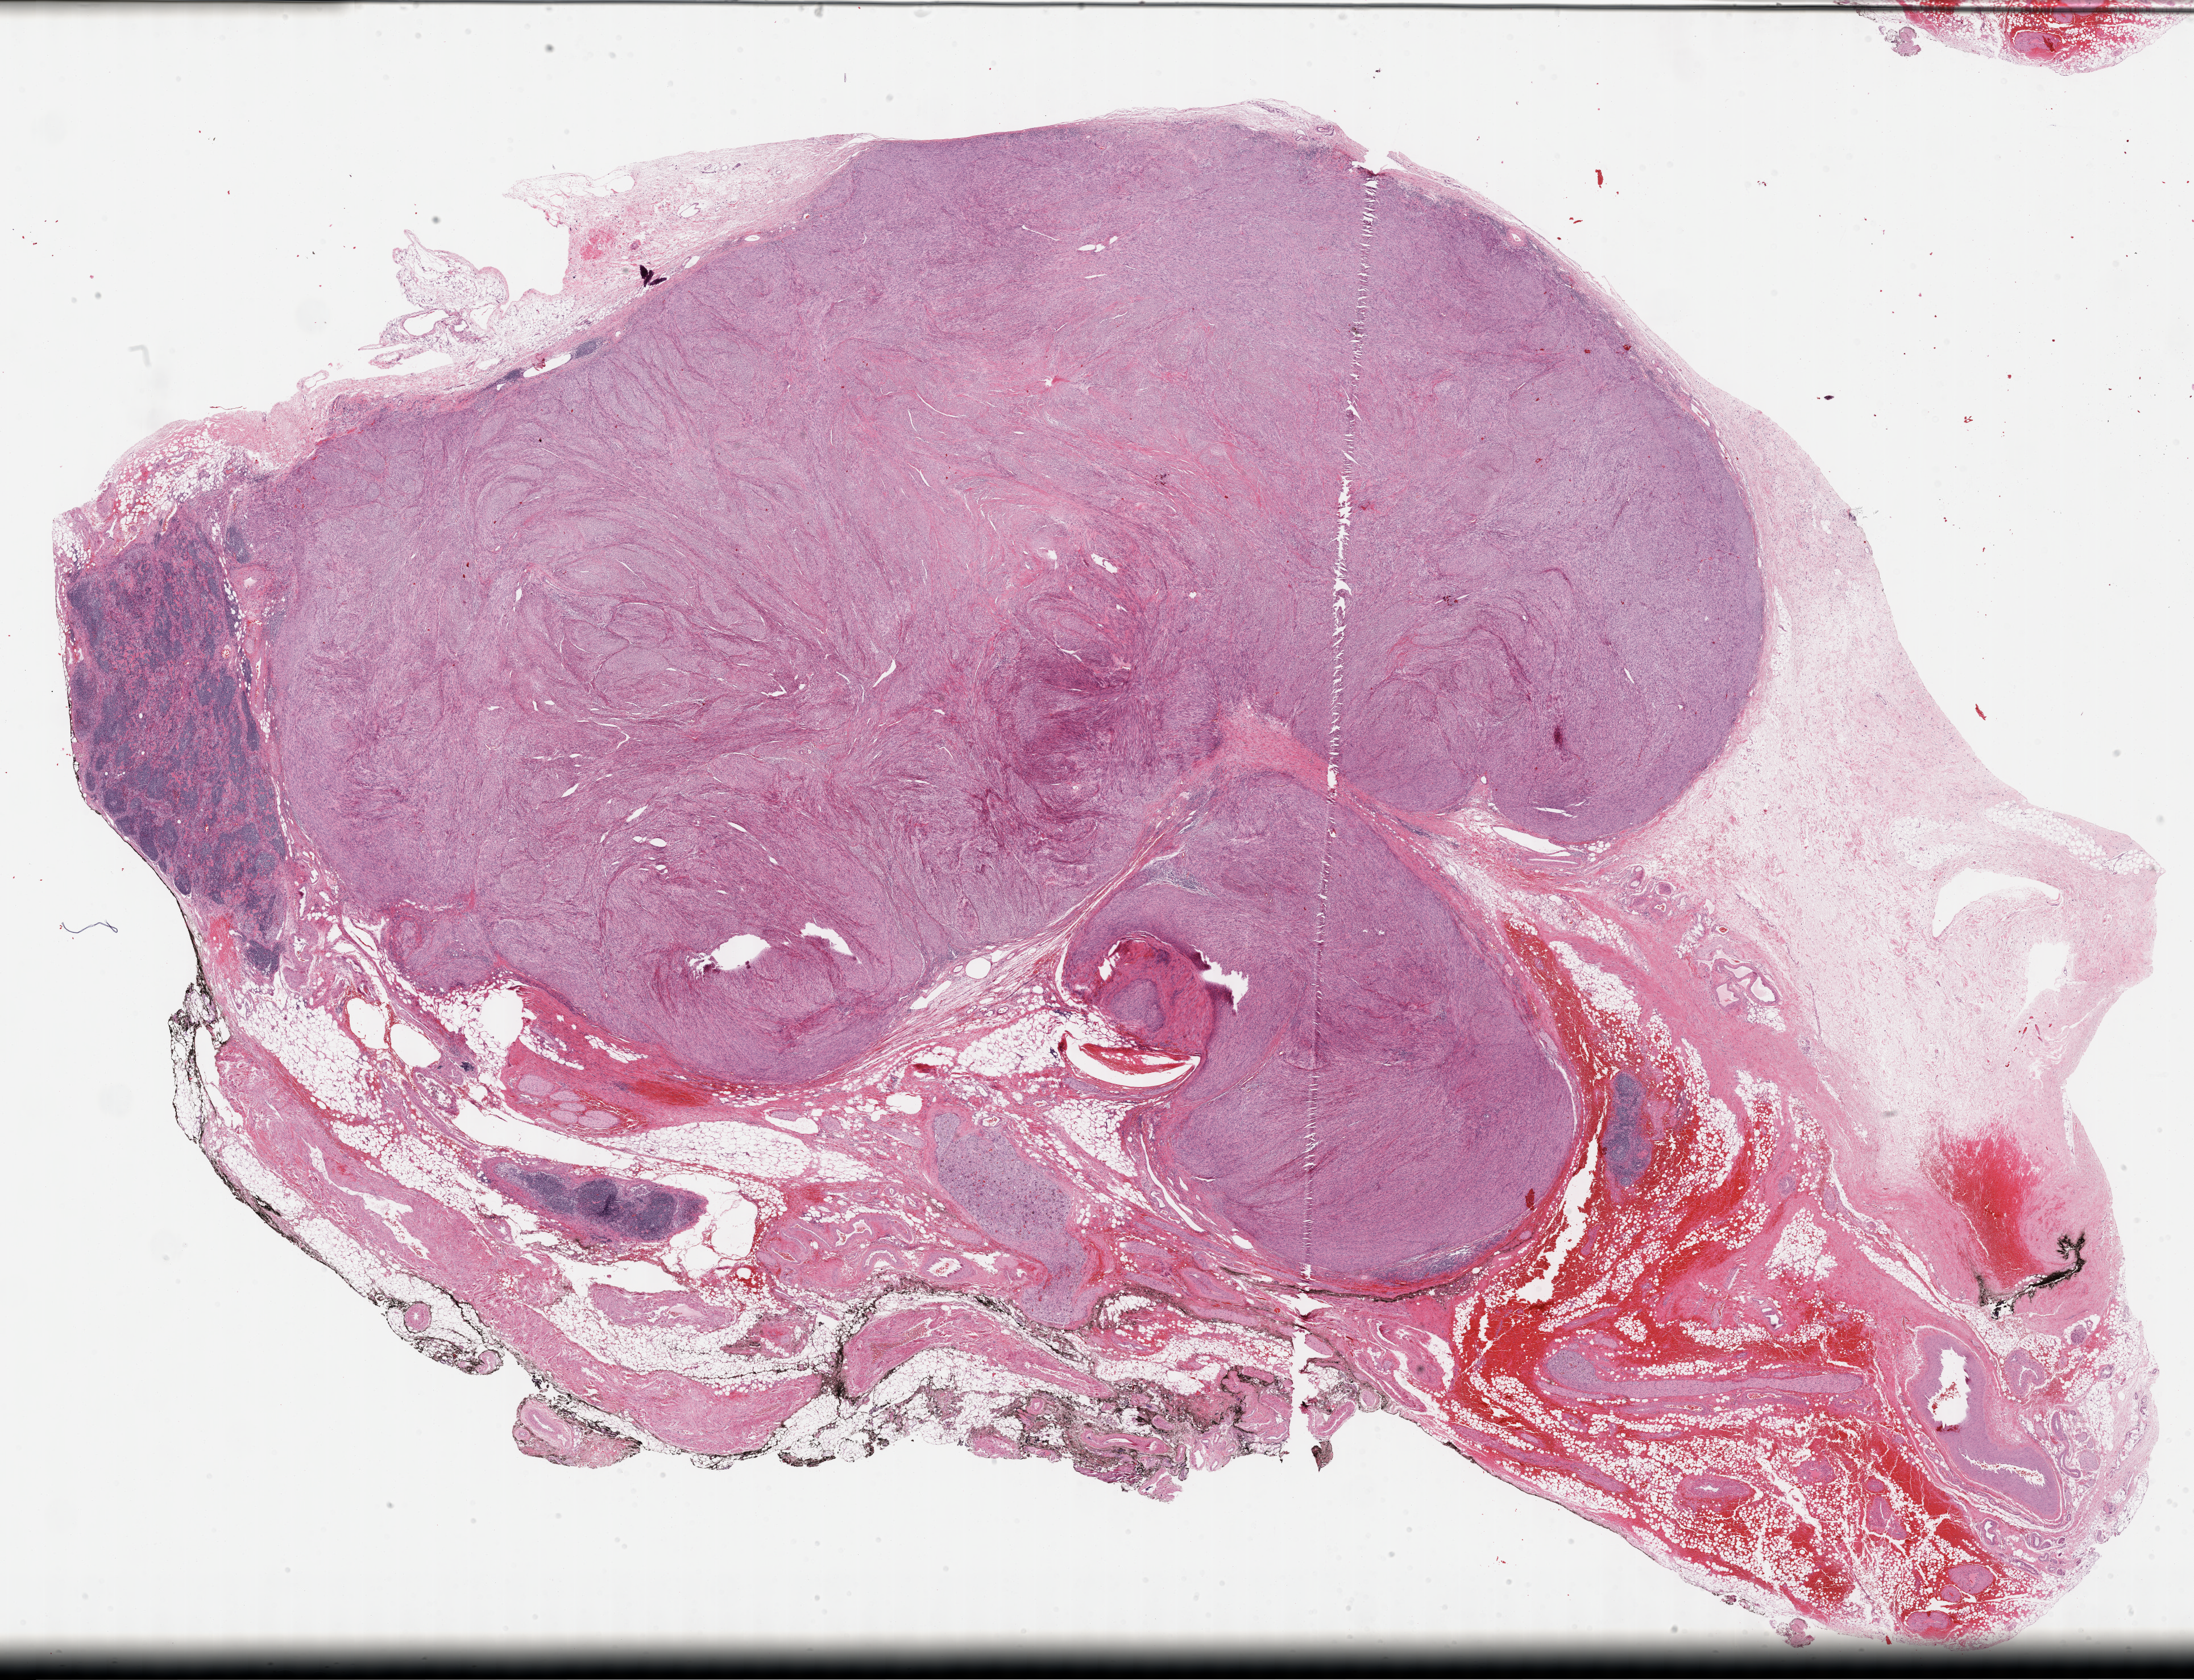
Digitized Hematoxylin and eosin (H&E) stained tissue section (whole slide), shown as a low-resolution overview of the whole scanned area (about 31.2 x 23.9 mm, acquisition: 40x scan); formalin-fixed paraffin-embedded (FFPE) diagnostic section; retroperitoneum and peritoneum, primary tumour sample. Female patient; age at initial diagnosis 78 years.
Pathologic diagnosis: Dedifferentiated liposarcoma (retroperitoneum).